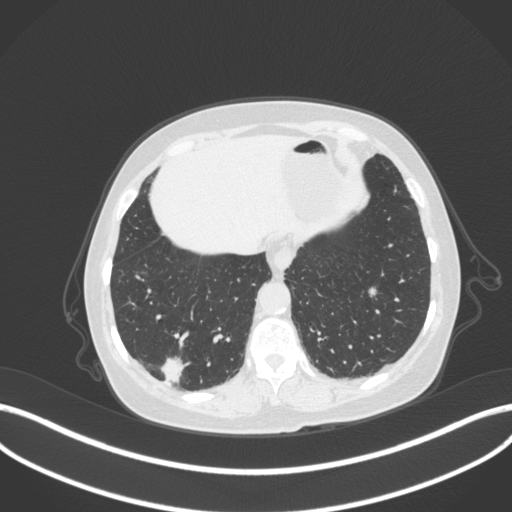
Chest CT, one axial slice; position 62 of 340 along the scan axis; reconstruction kernel B31f; 120 kVp; lung window (W 1500 / L -600 HU); 1 mm slice thickness; 512 × 512 image matrix, field of view 400 × 400 mm. Female patient, age 69 years. Case-level facts recorded for this patient, not image findings: clinical TNM (as recorded): T1b N0 M0; histopathological grade: G2-3.
Outlined on this slice (bounding box drawn by a radiologist):
- lung tumour (recorded histology: adenocarcinoma): bounding box [x1, y1, x2, y2] px = [158, 352, 190, 387]